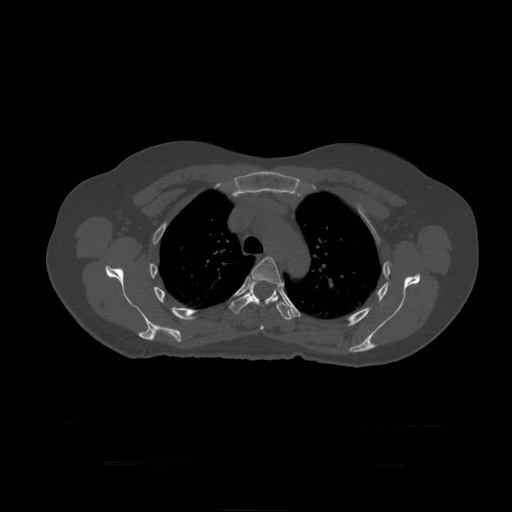
CT including the spine, one axial slice; slice 327 of 399 in the series (ordered by position); 120 kVp; bone window (W 1800 / L 400 HU); 1.25 mm slice thickness; 512 × 512 image matrix. Patient age 41 years. Case-level facts recorded for this patient, not image findings: primary cancer: breast.
Outlined on this slice (semi-automatically segmented with operator editing):
- T5 vertebra: bounding box (x1, y1, x2, y2) in pixels: (241, 257, 281, 330)
- T6 vertebra: (230, 280, 296, 320)